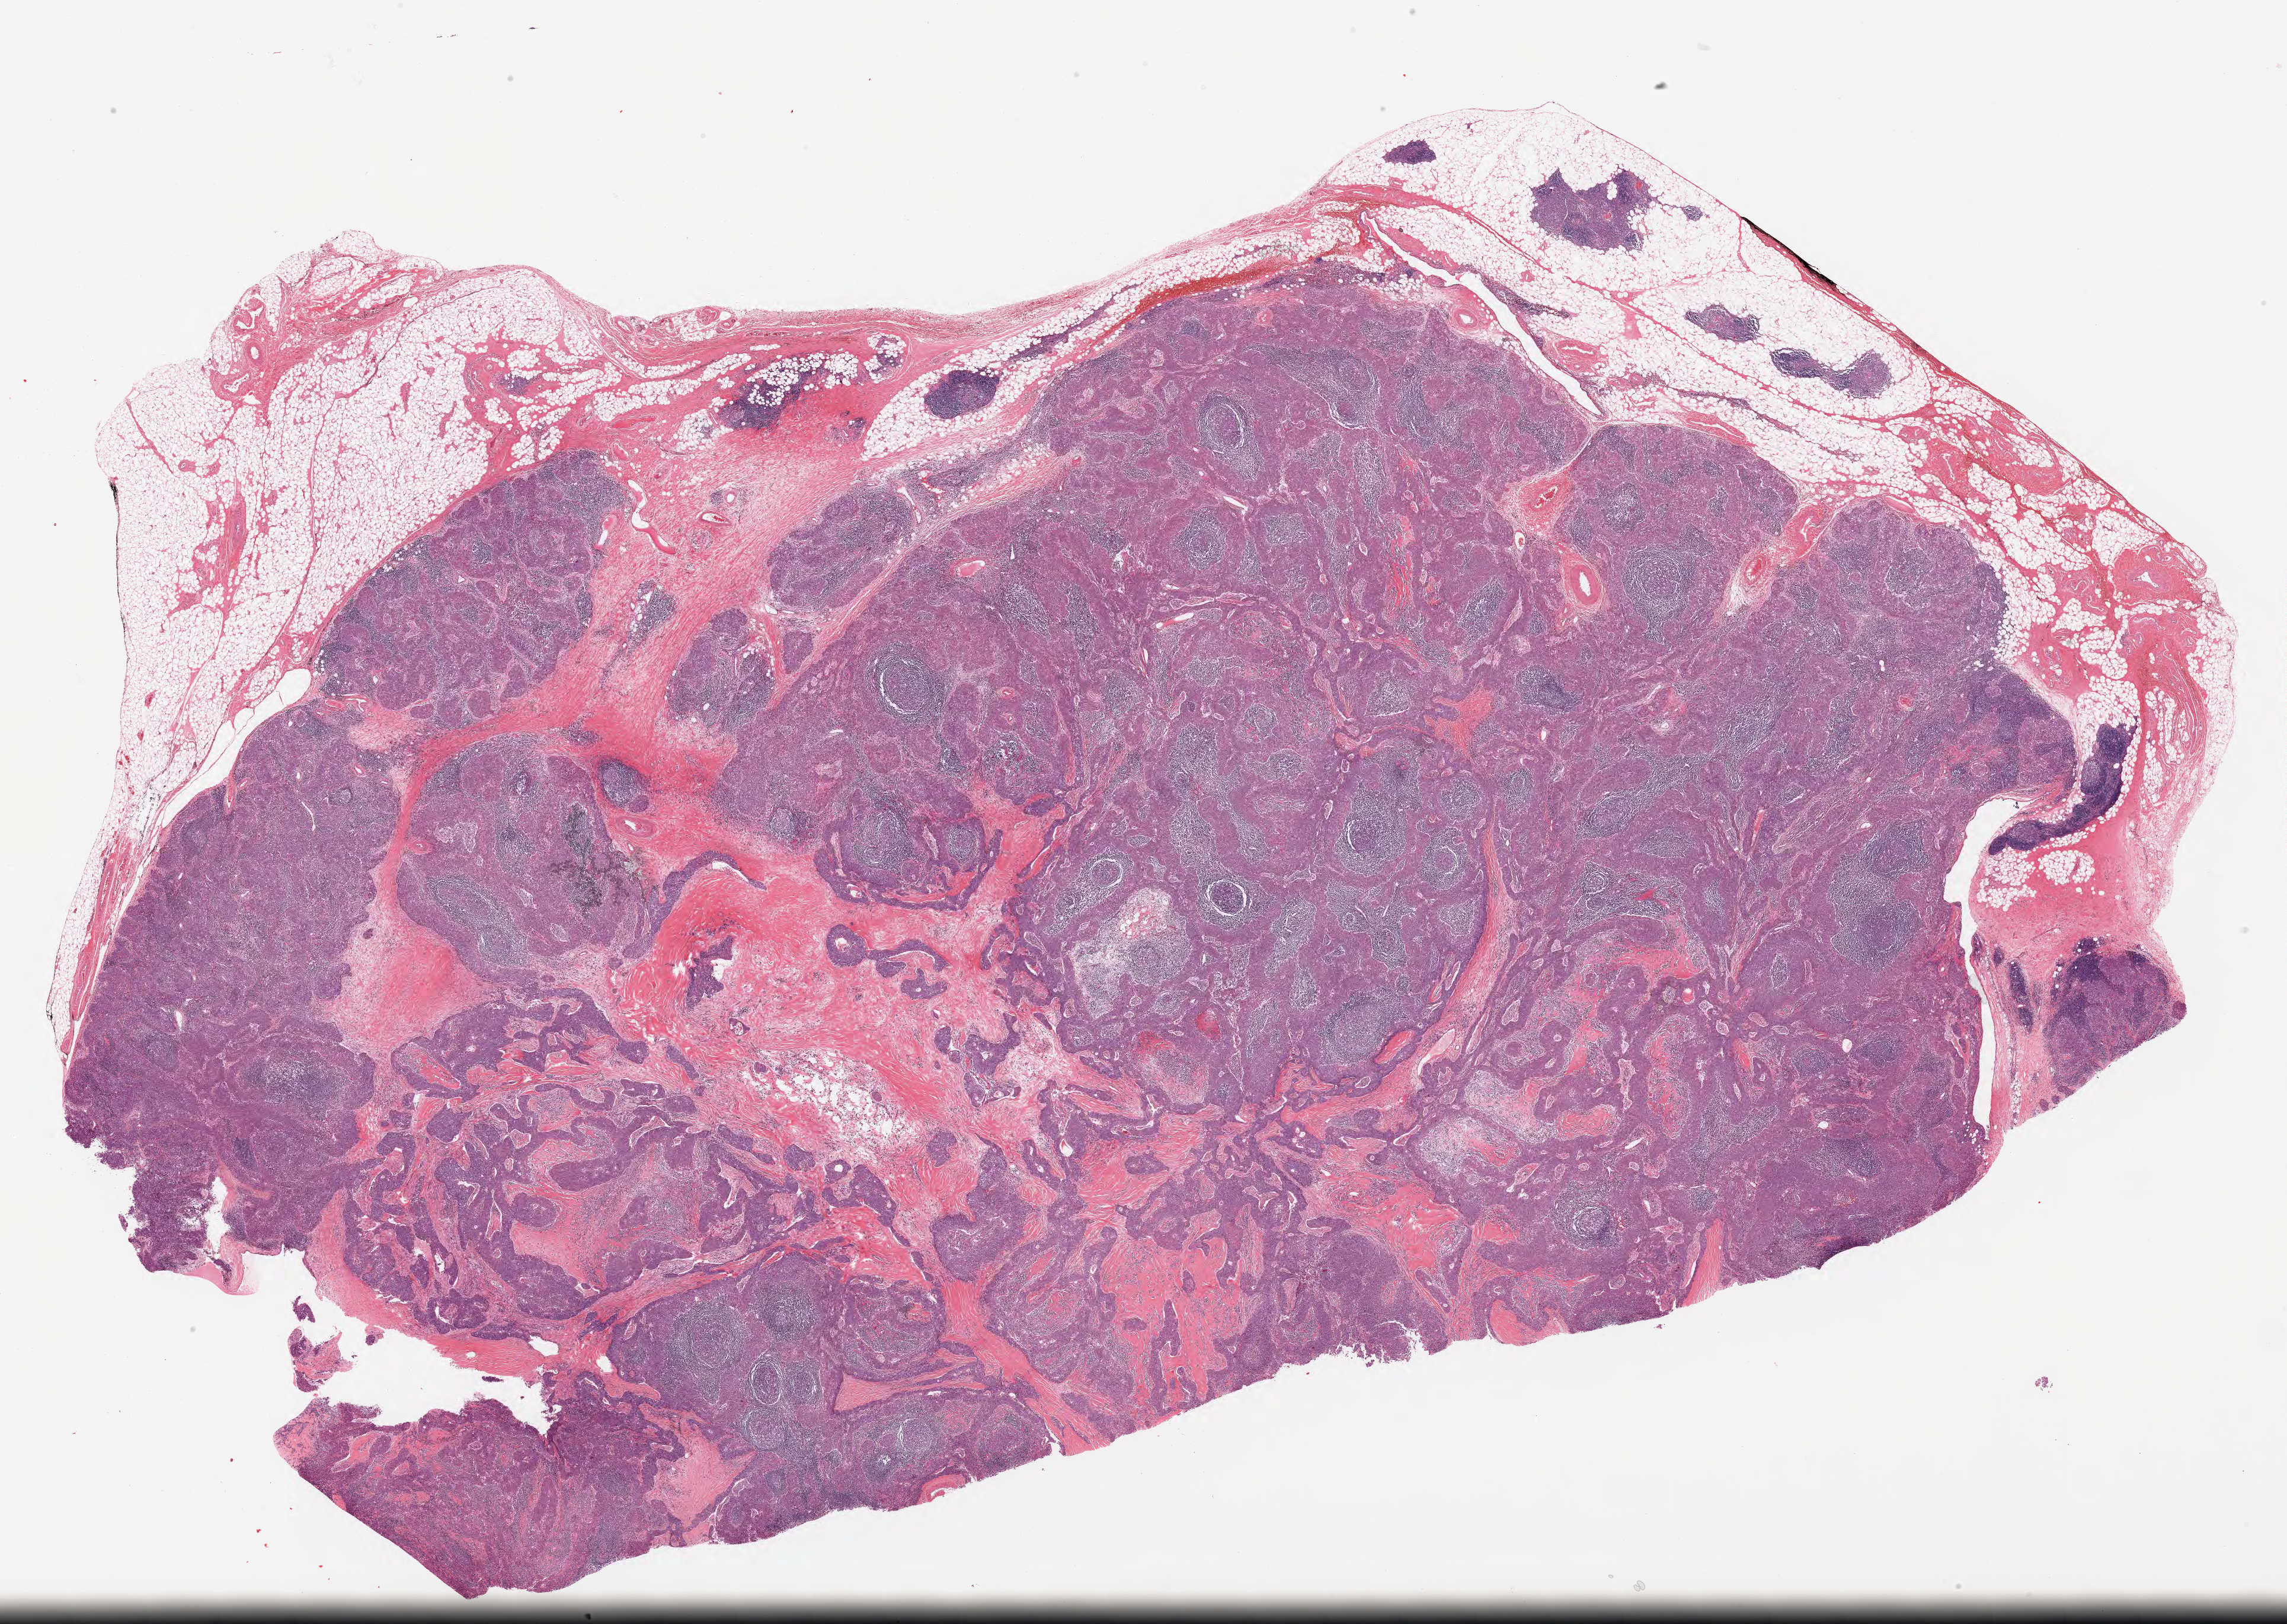
Hematoxylin and eosin (H&E) stained whole-slide image — whole scanned area (about 30.5 x 21.6 mm) shown as a low-resolution overview; formalin-fixed paraffin-embedded (FFPE) diagnostic section; thymus, primary tumour sample. Patient: female, age at initial diagnosis 52 years.
• pathologic diagnosis: Thymic carcinoma, NOS